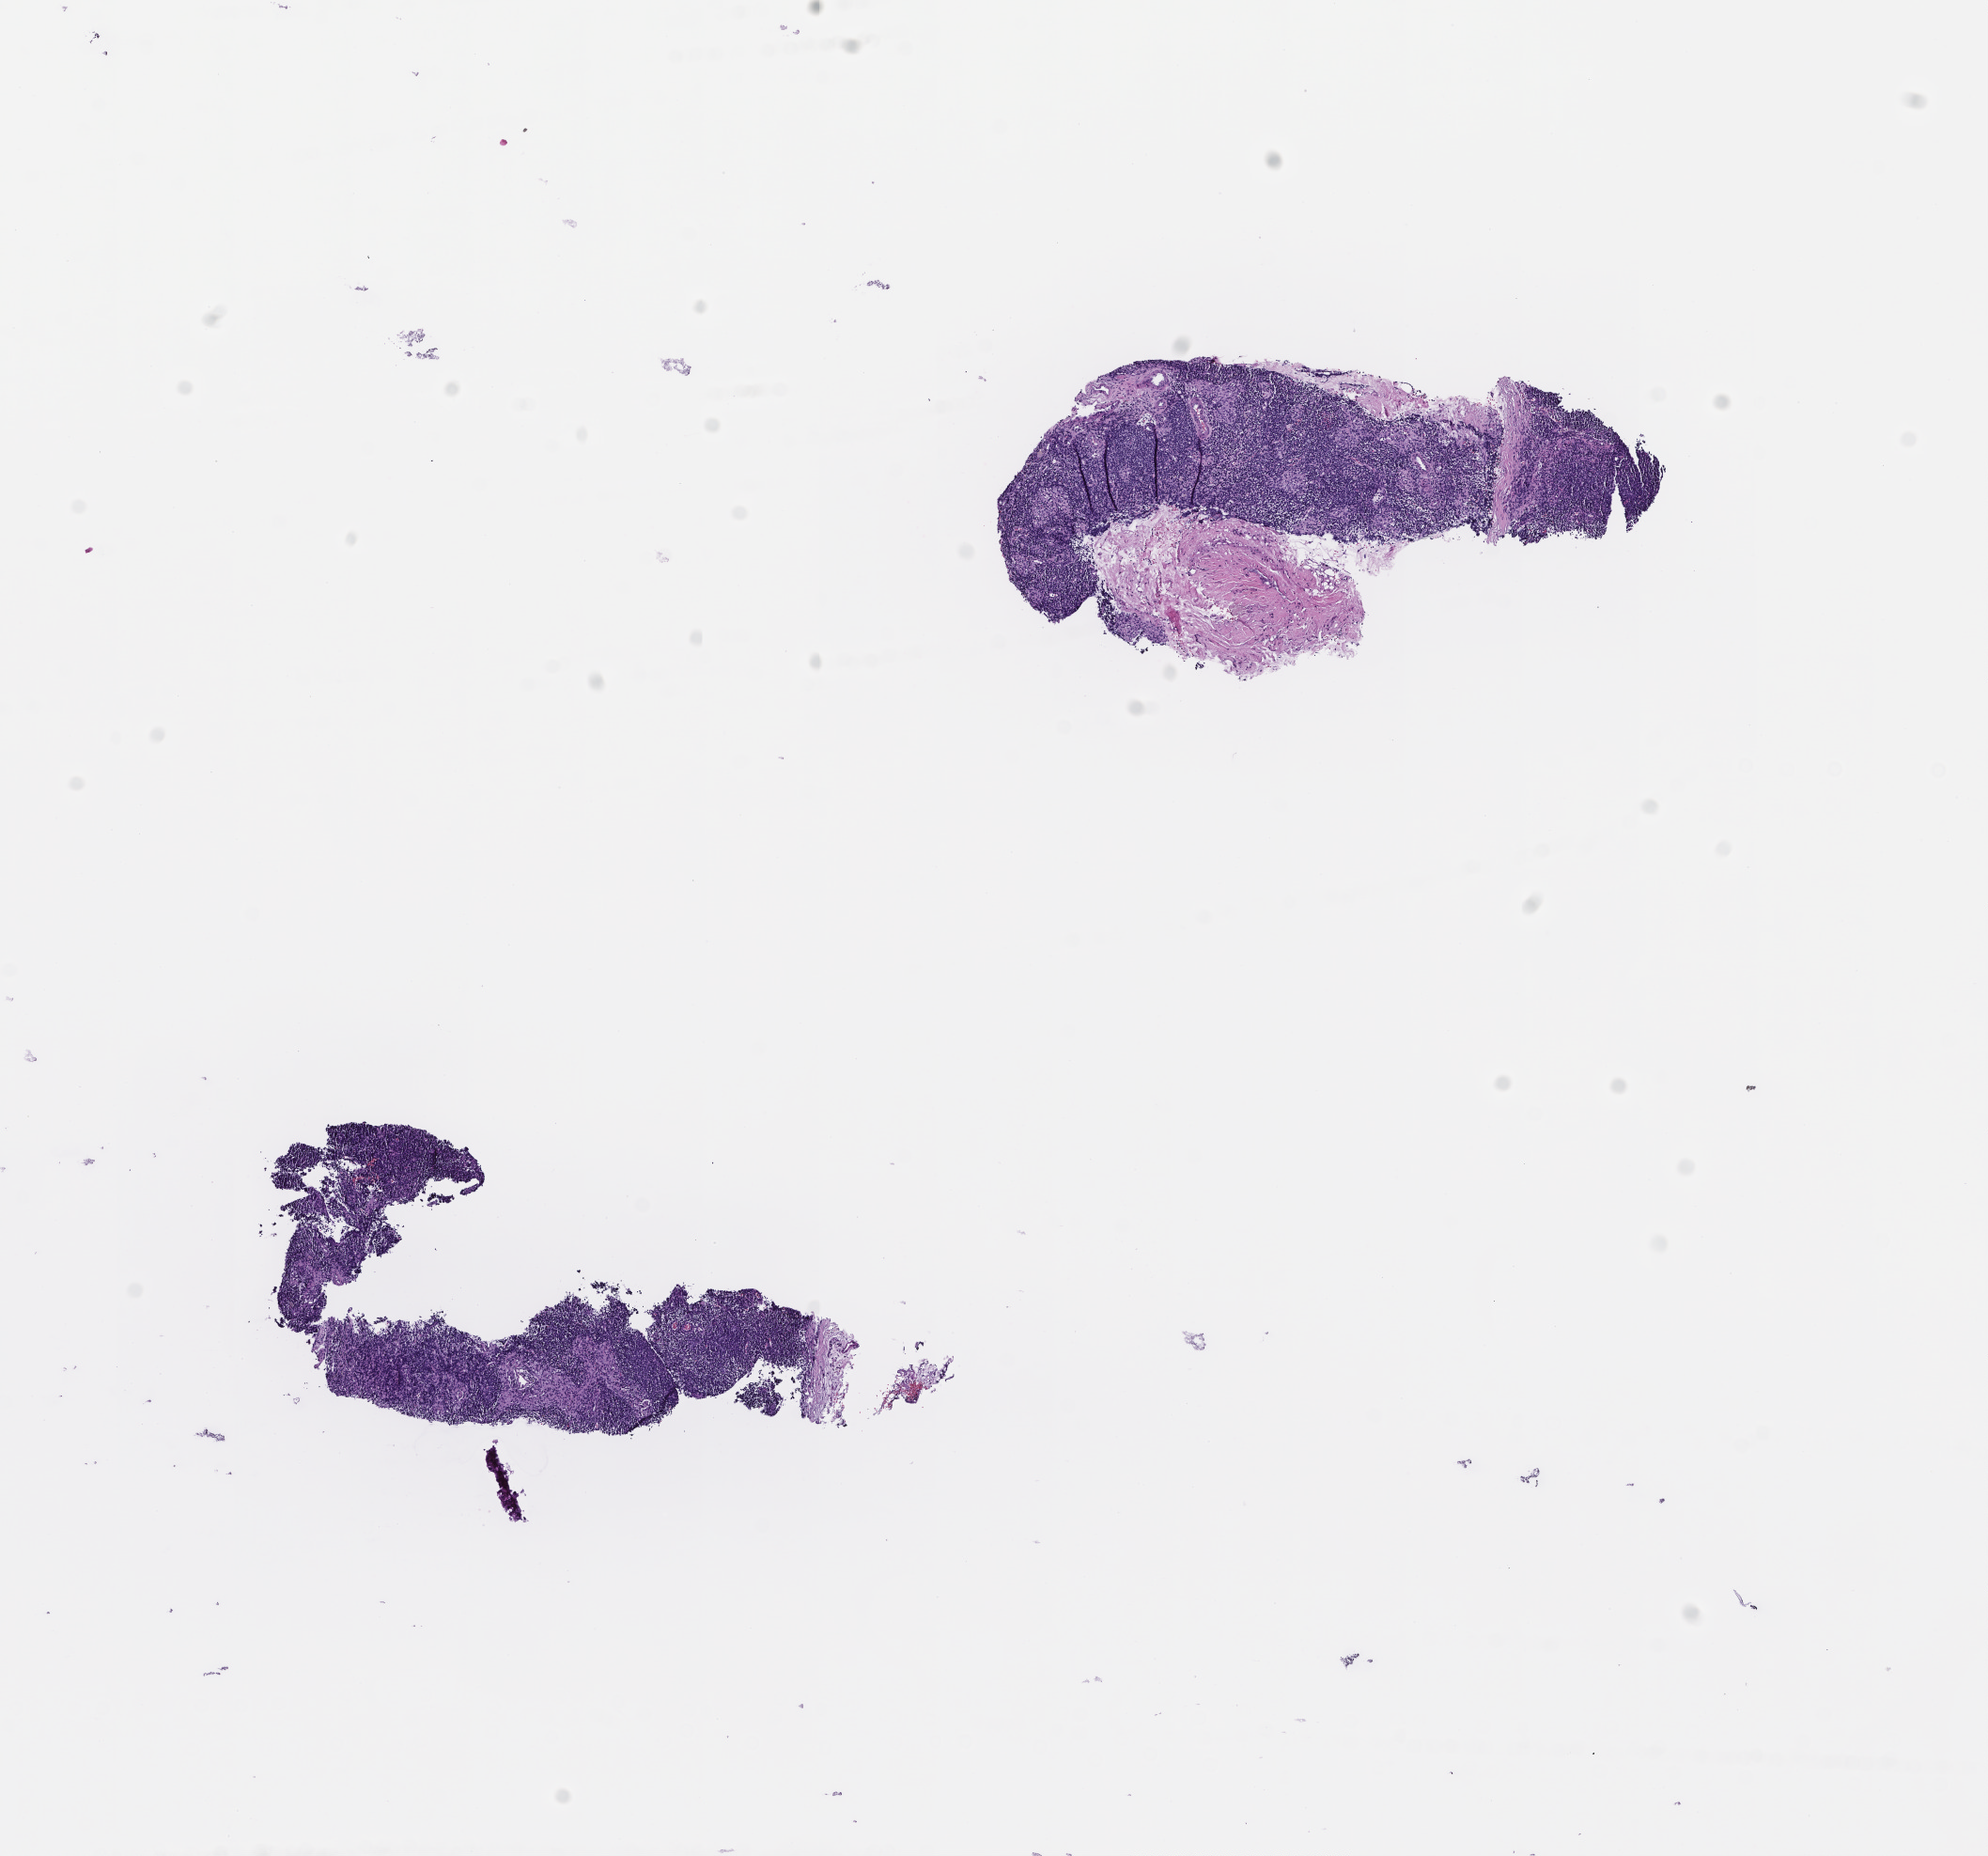
Whole-slide image, haematoxylin and eosin stain — low-resolution overview of the scanned area, about 8.5 x 8.0 mm, FFPE section. Patient sex: male.
This section: metastasis (sampled organ not recorded). Primary diagnosis of the patient: Melanoma.